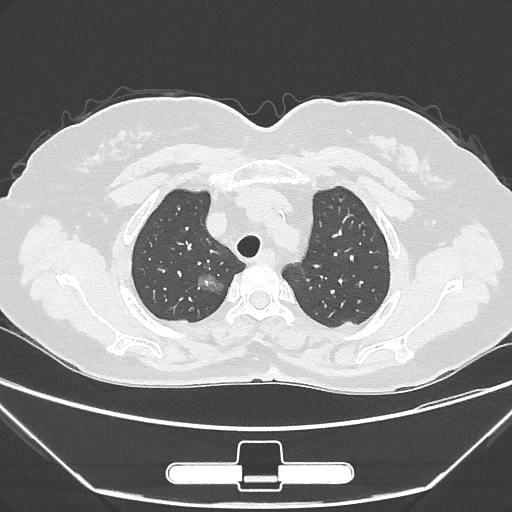
Chest CT, one axial slice; slice 229 of 275 in the series (ordered by position); reconstruction kernel IMR1,SharpPlus; 120 kVp; lung window (W 1500 / L -600 HU); 1 mm slice thickness; 512 × 512 image matrix, field of view 356 × 356 mm. Female patient, age 63 years. Case-level facts recorded for this patient, not image findings: clinical TNM (as recorded): T1a N0 M0.
Annotated regions visible in this slice (bounding box drawn by a radiologist):
- lung tumour (recorded histology: adenocarcinoma): bounding box [x1, y1, x2, y2] px = [189, 266, 224, 298]